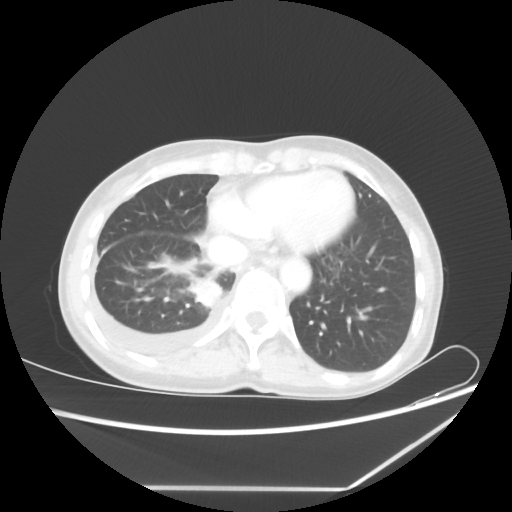
Chest CT, one axial slice. Position 18 of 60 along the scan axis. 80 kVp. Lung window (W 1500 / L -600 HU). 512 × 512 image matrix, field of view 364 × 364 mm. Patient: female, 59 years. Case-level facts recorded for this patient, not image findings: clinical TNM (as recorded): T1c N1 M1.
Structures marked on this image (rectangle marked by the reading radiologist):
- lung tumour (recorded histology: adenocarcinoma): bounding box [x1, y1, x2, y2] px = [188, 275, 223, 309]